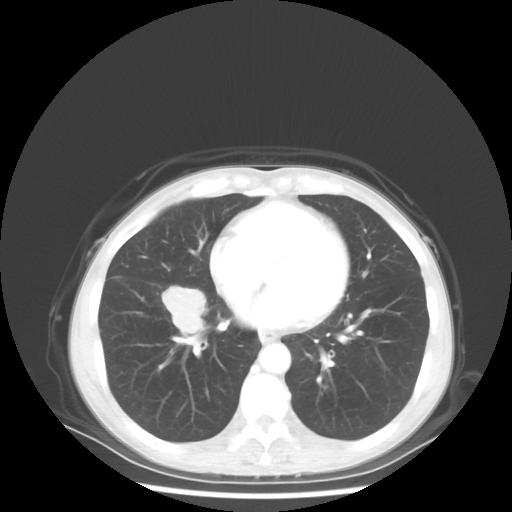
Chest CT, one axial slice; slice 21 of 56 in the series (ordered by position); lung window (W 1500 / L -600 HU); 512 × 512 image matrix, field of view 360 × 360 mm. Patient: female, 57 years. From the clinical record (not read from this slice): clinical TNM (as recorded): T1c N3 M1a; histopathological grade: G3.
Structures marked on this image (rectangle marked by the reading radiologist):
- lung tumour (recorded histology: adenocarcinoma): bounding box [x1, y1, x2, y2] px = [160, 283, 207, 336]